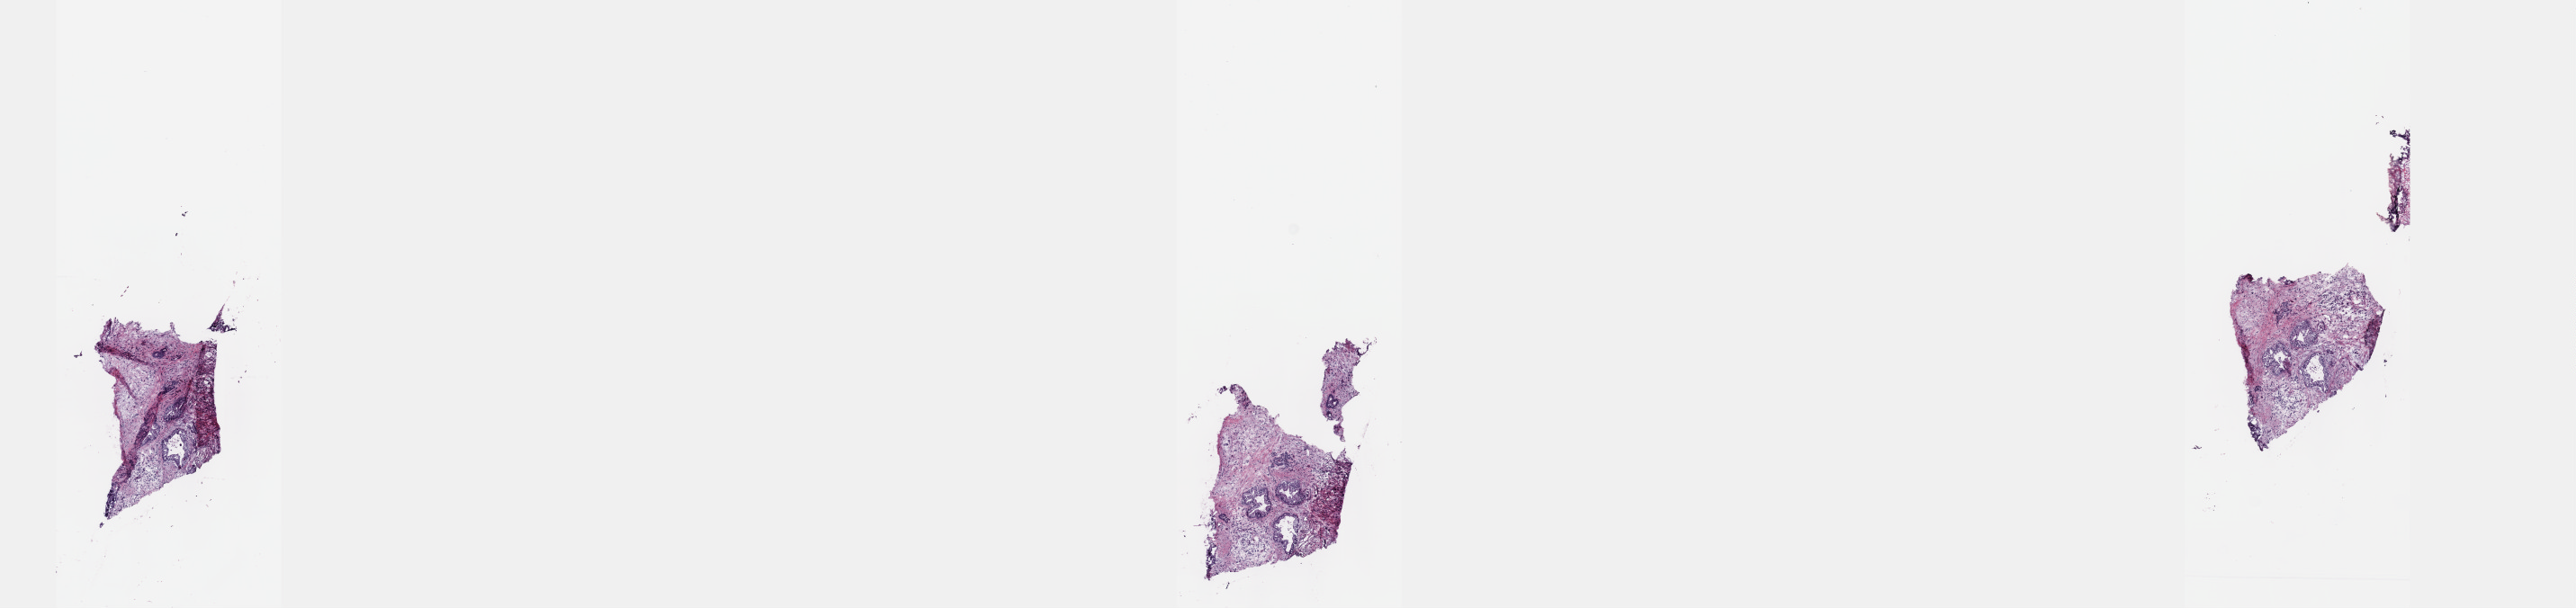
Digitized H&E tissue section (whole slide) — whole scanned area (about 23.1 x 5.5 mm, acquisition: 40x scan) shown as a low-resolution overview; frozen section; pancreas, primary tumour sample. Patient: female, age at initial diagnosis 75 years. Histologic grade: G2 (moderately differentiated). Pathologist review of this section (percent, as recorded): tumour cells 22%, tumour nuclei 80%, normal cells 3%, stromal cells 72%, necrosis 3%. Inflammatory infiltration, as recorded: lymphocyte infiltration 10%, monocyte infiltration 0%, neutrophil infiltration 0%.
- AJCC pathologic stage: IIB
- lymph nodes positive (case pathology): 3 of 11 examined
- histologic diagnosis: Infiltrating duct carcinoma, NOS (body of pancreas)